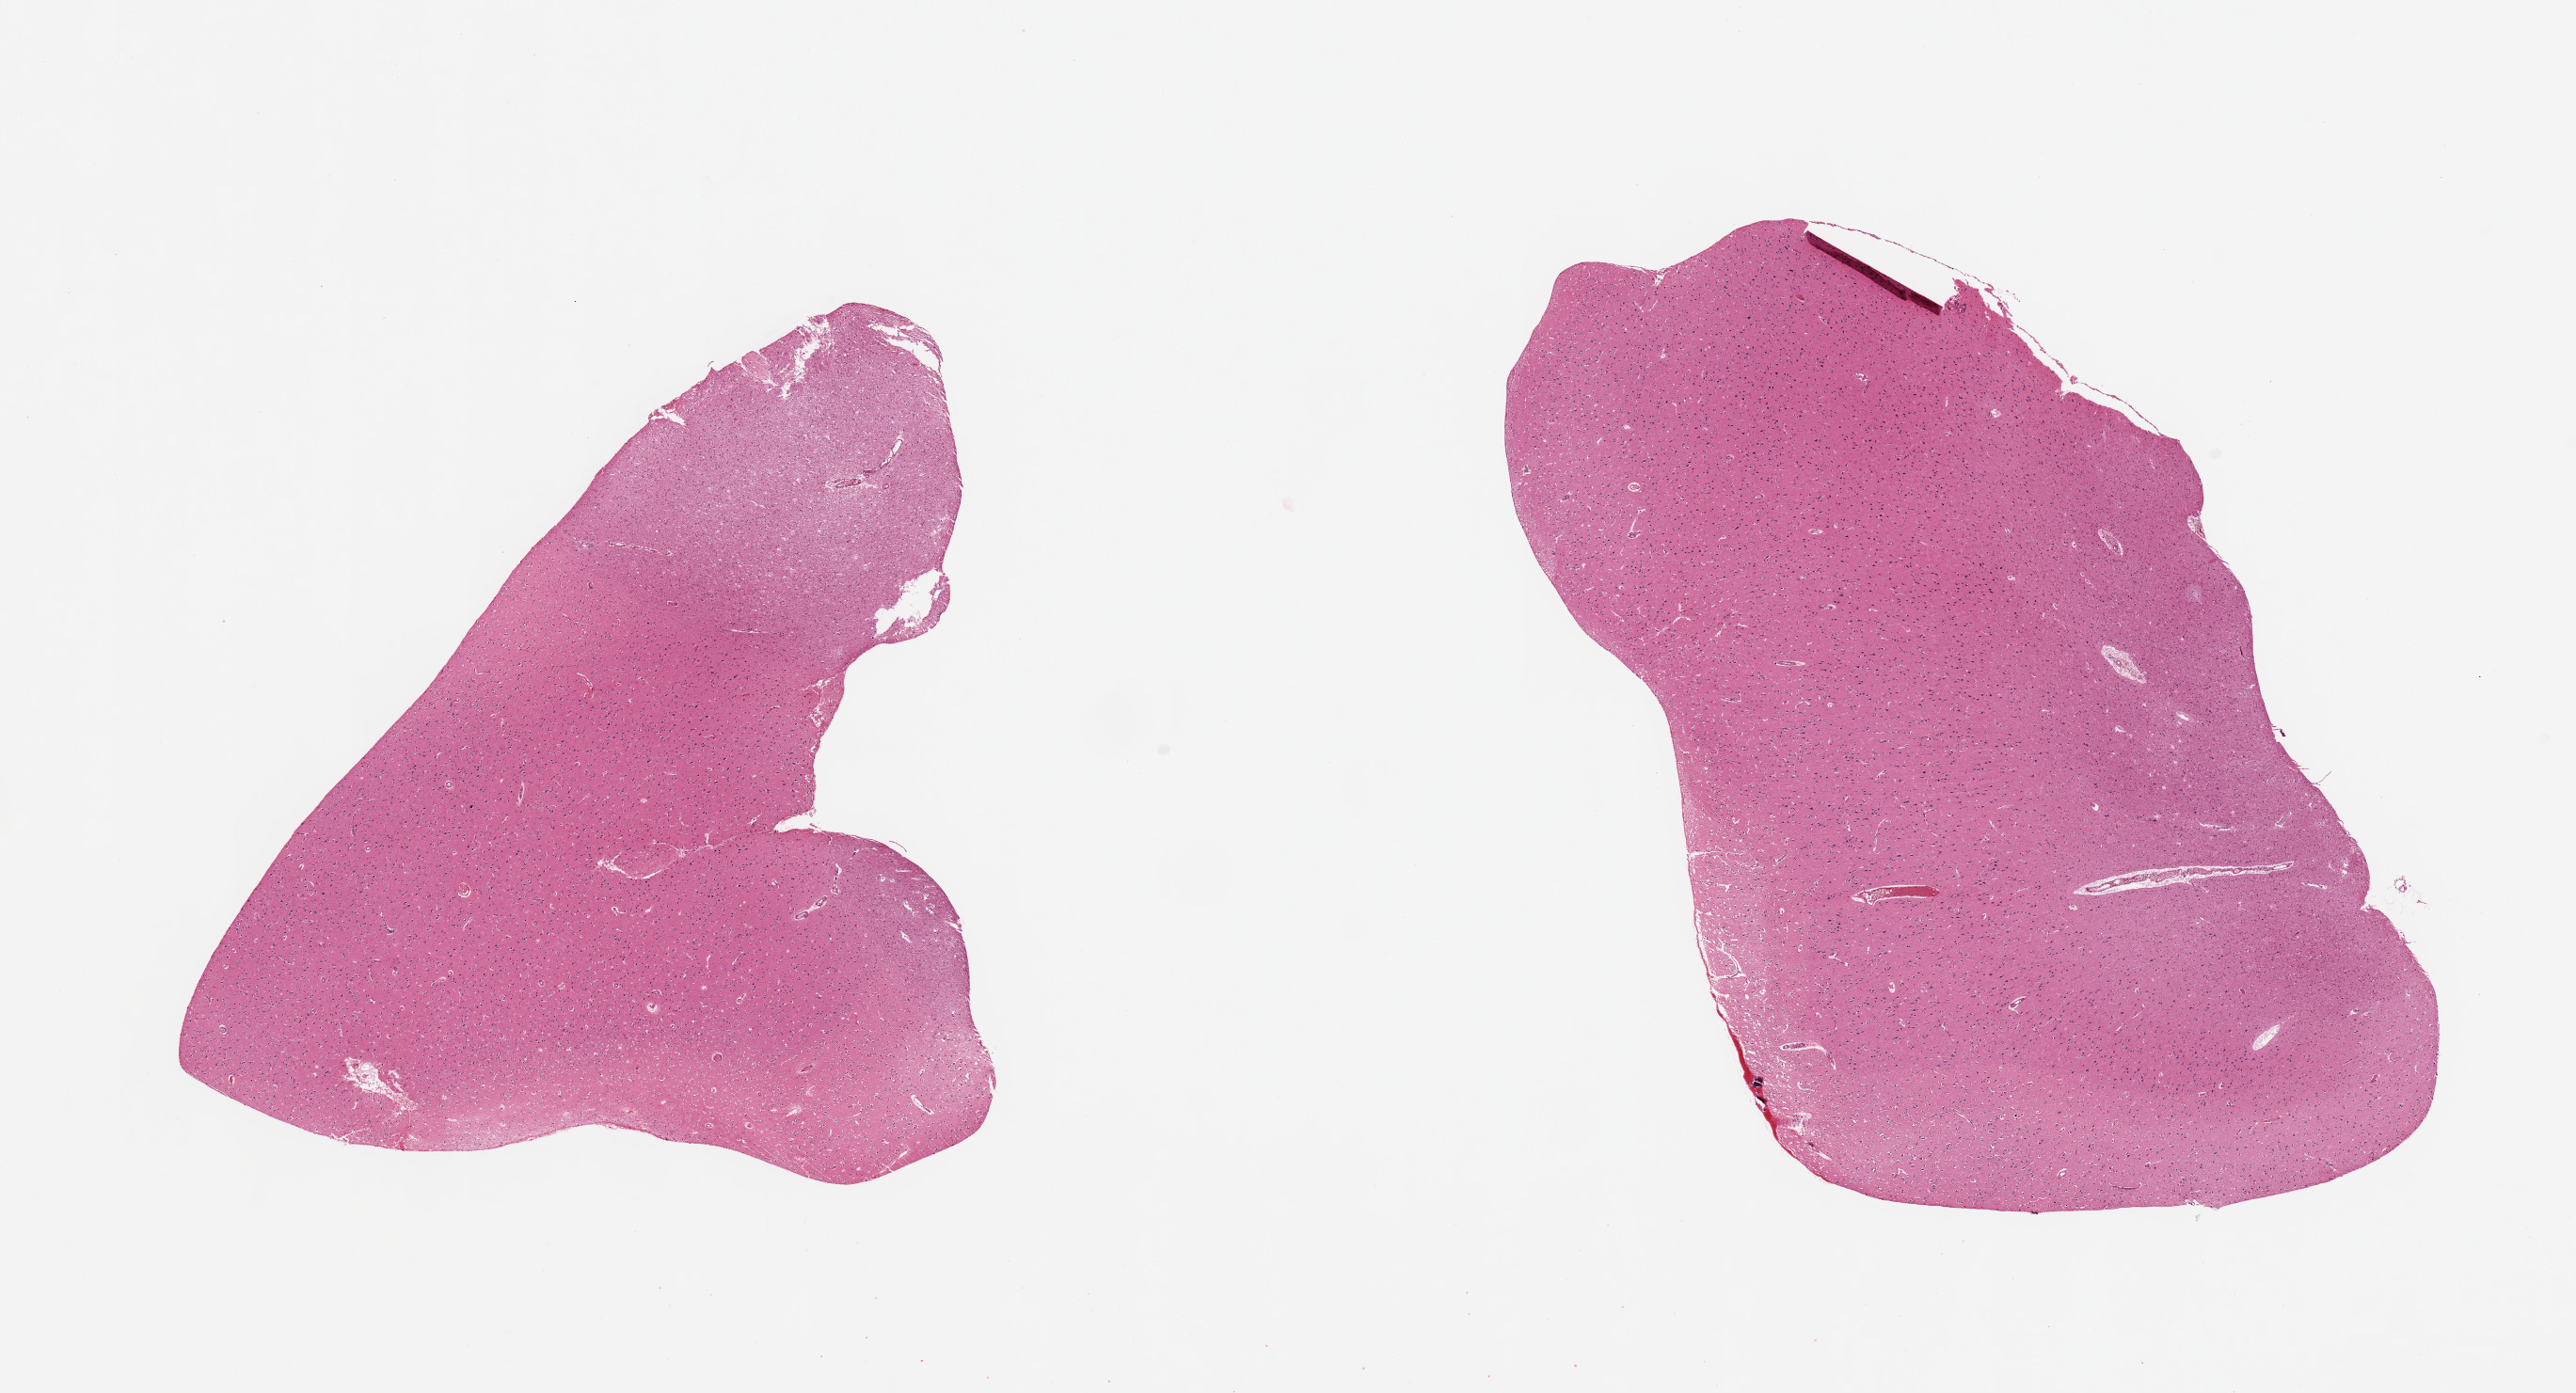
Whole-slide image, H&E stain, a low-resolution overview of the entire scanned area, about 21.7 x 11.7 mm (from a 20x scan), PAXgene-fixed, paraffin-embedded tissue, sampled site (target tissue): cerebral cortex, donor tissue sample. Female donor.
- review note (as recorded): 2 pieces, no abnormalities